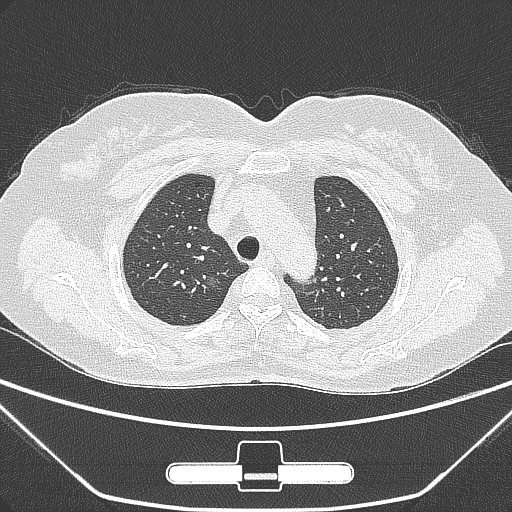
Chest CT, one axial slice; position 222 of 275 along the scan axis; lung window (W 1500 / L -600 HU); 1 mm slice thickness; 512 × 512 image matrix. Patient: female, 63 years. Case-level facts recorded for this patient, not image findings: clinical TNM (as recorded): T1a N0 M0; histopathological grade: G1.
Outlined on this slice (rectangle marked by the reading radiologist):
- lung tumour (recorded histology: adenocarcinoma): box from (x=198, y=271) to (x=227, y=294) px